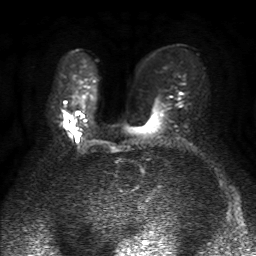
Breast MRI, one axial slice. Diffusion-weighted series; image 2 of 4 stored at this slice position (different b-values; order by instance number). 1.5 T. 4 mm slice thickness. 256 × 256 image matrix, field of view 320 × 320 mm. Female patient.
Outlined on this slice (expert manual segmentation):
- tumour on diffusion-weighted imaging: bounding box <66,115,73,130> (left, top, right, bottom; pixels)